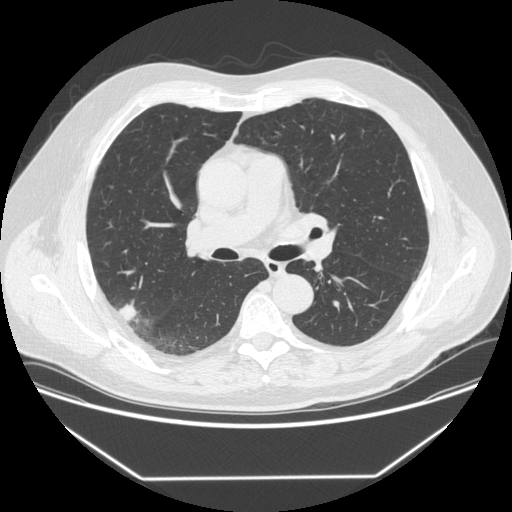
Low-dose screening chest CT, one axial slice; slice 213 of 342 in the series (ordered by position); lung window (W 1500 / L -600 HU); 512 × 512 image matrix, field of view 410 × 410 mm.
Outlined on this slice (outlined manually by an expert reader):
- lesion 1 (tumor, upper lobe of right lung): bounding box [x1, y1, x2, y2] px = [118, 304, 137, 321]